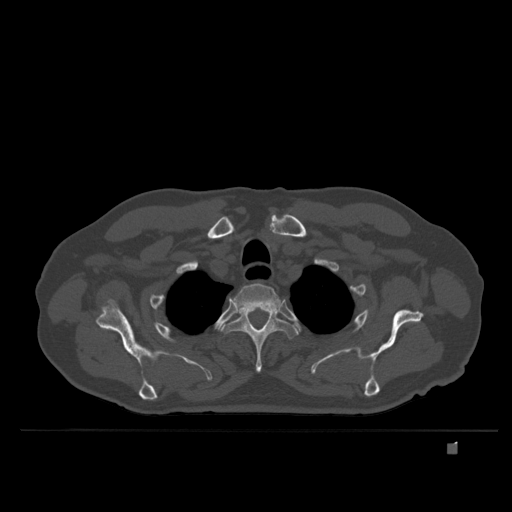
CT including the spine, one axial slice; slice 304 of 435 in the series (ordered by position); bone window (W 1800 / L 400 HU); 1.5 mm slice thickness; 512 × 512 image matrix, field of view 434 × 434 mm. Male patient, age 73 years. Case-level facts recorded for this patient, not image findings: primary cancer: skin.
Annotated regions visible in this slice (semi-automatic segmentation, software-assisted and operator-edited):
- T2 vertebra: bounding box [x1, y1, x2, y2] px = [230, 283, 281, 310]
- T3 vertebra: [221, 306, 299, 373]